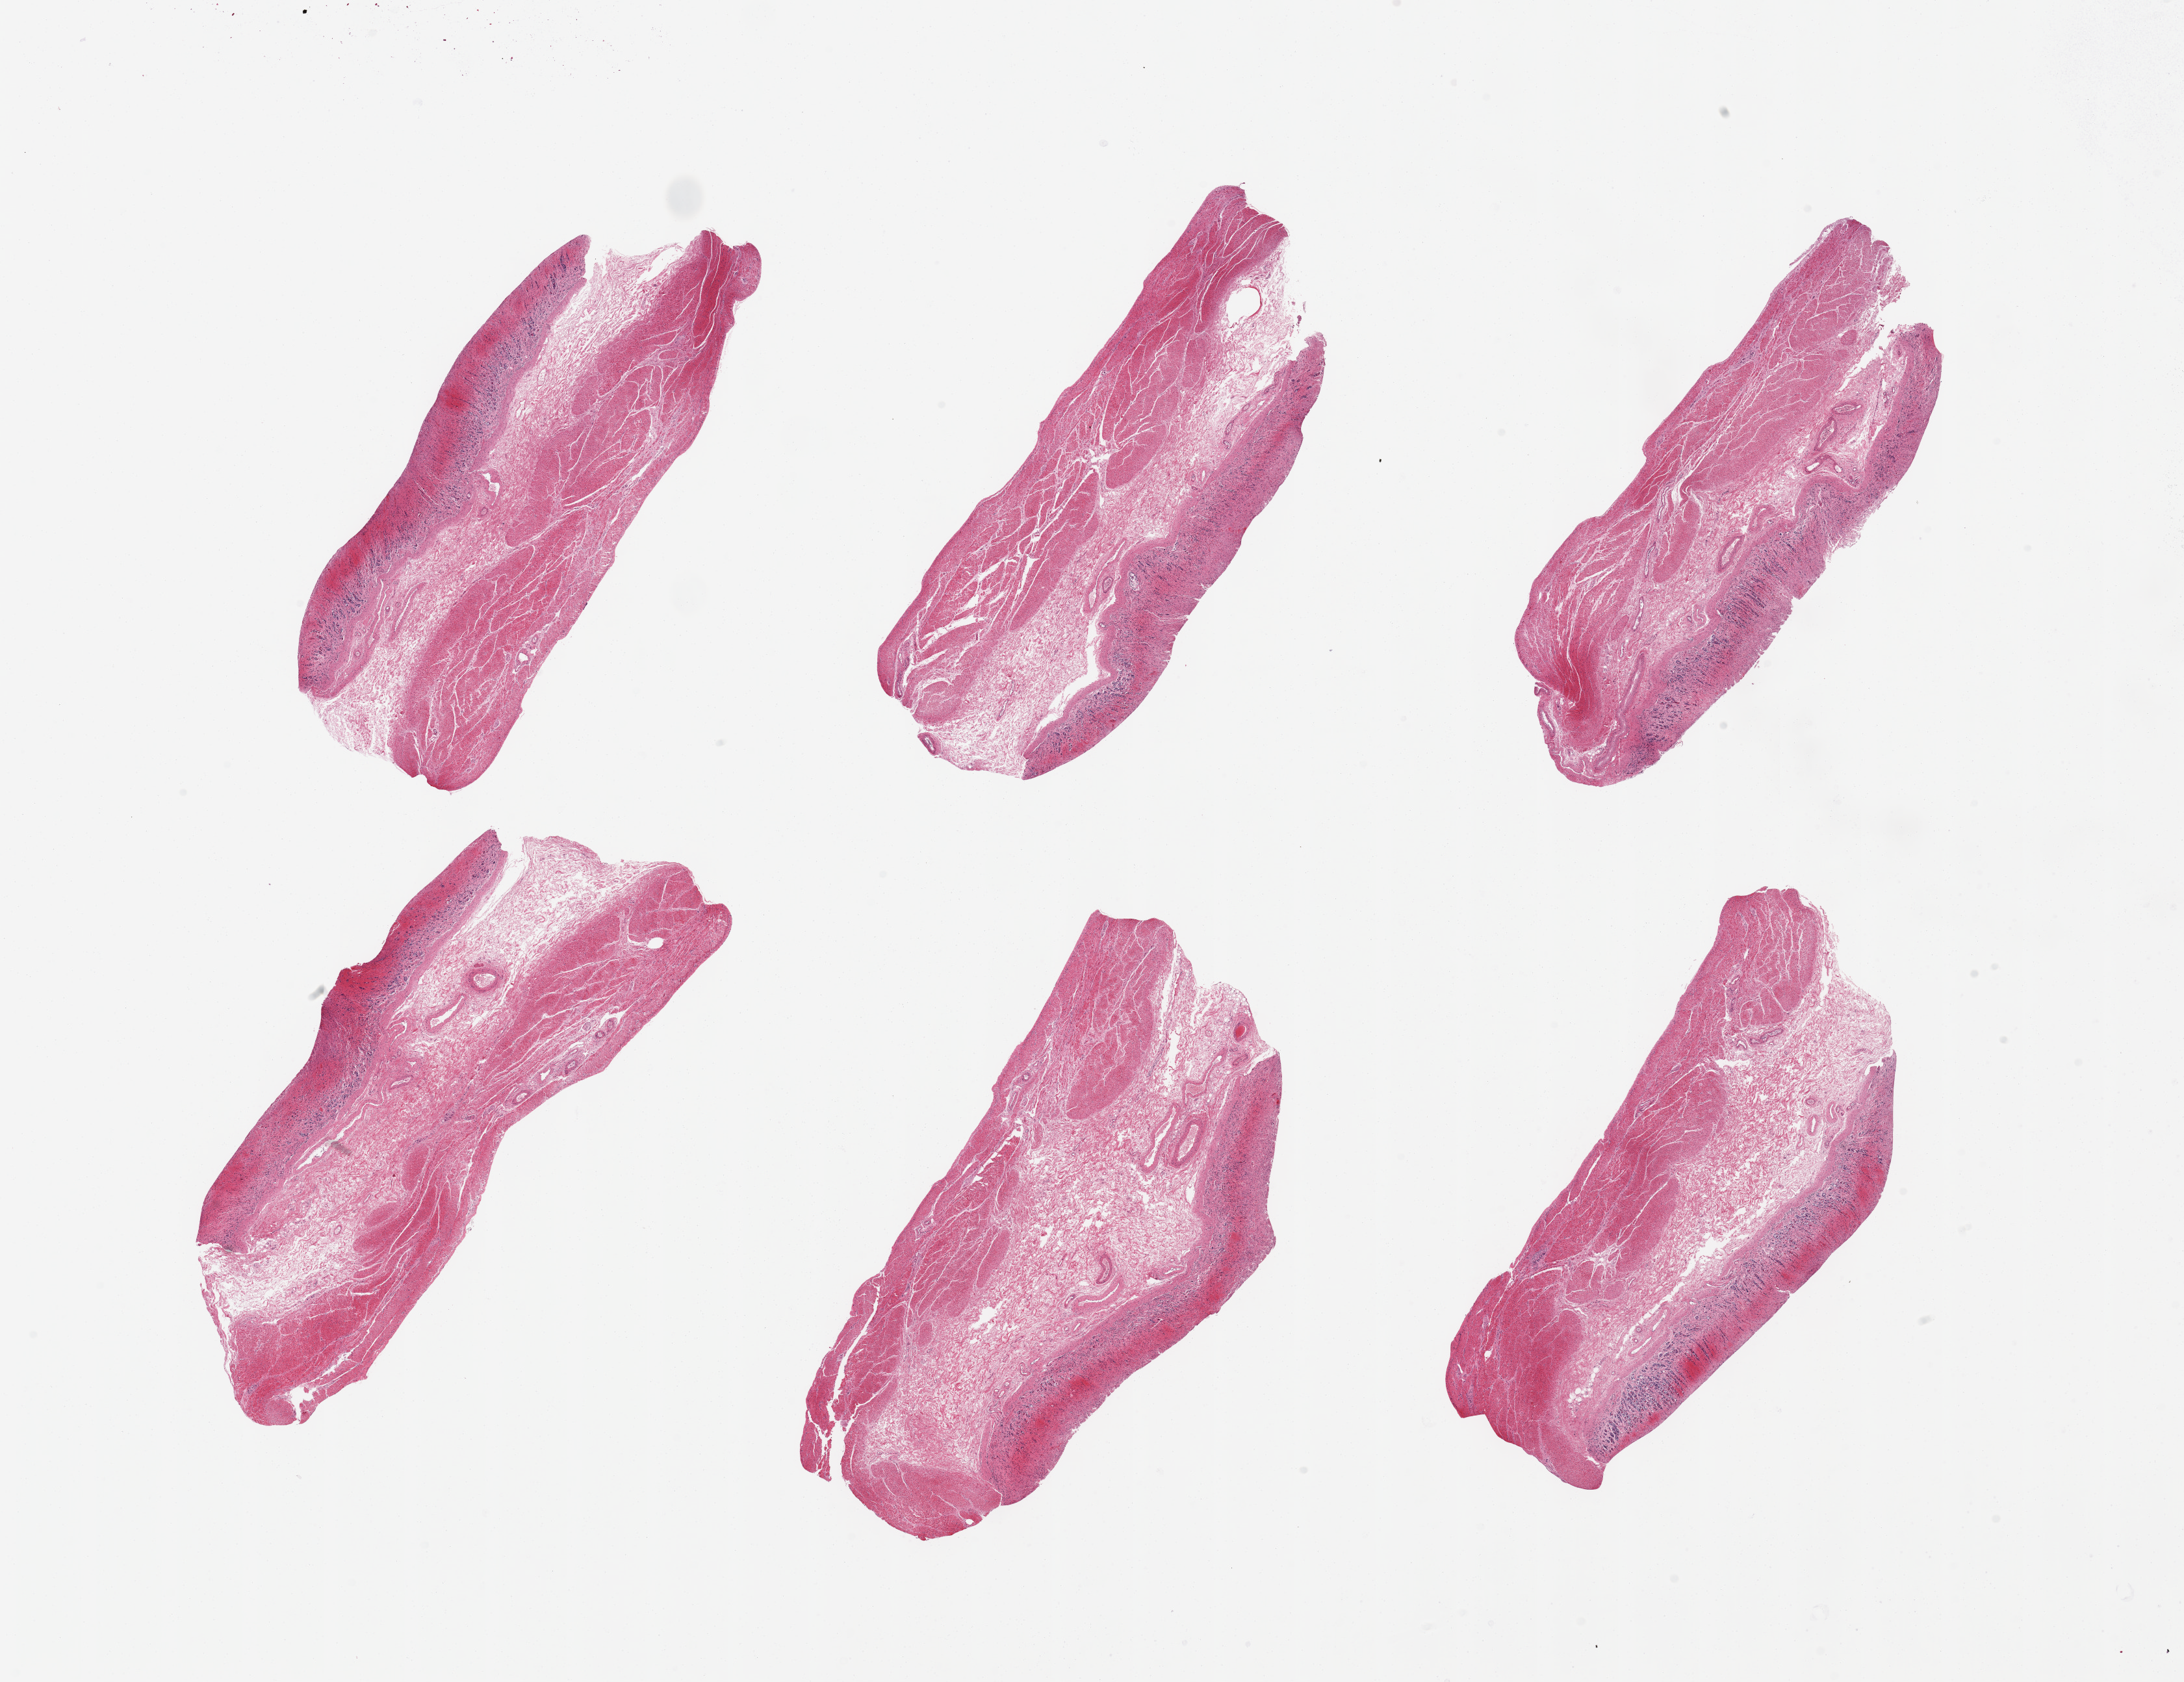
H&E whole-slide image, whole scanned area (about 26.6 x 20.5 mm) shown as a low-resolution overview. PAXgene-fixed, paraffin-embedded tissue. Sampled site (target tissue): stomach. Tissue donor sample. Donor: female.
Pathologist's review note for this sample: 6 pieces, mucosa up to ~1mm, advanced autolysis, glandular elments largely sloughed.